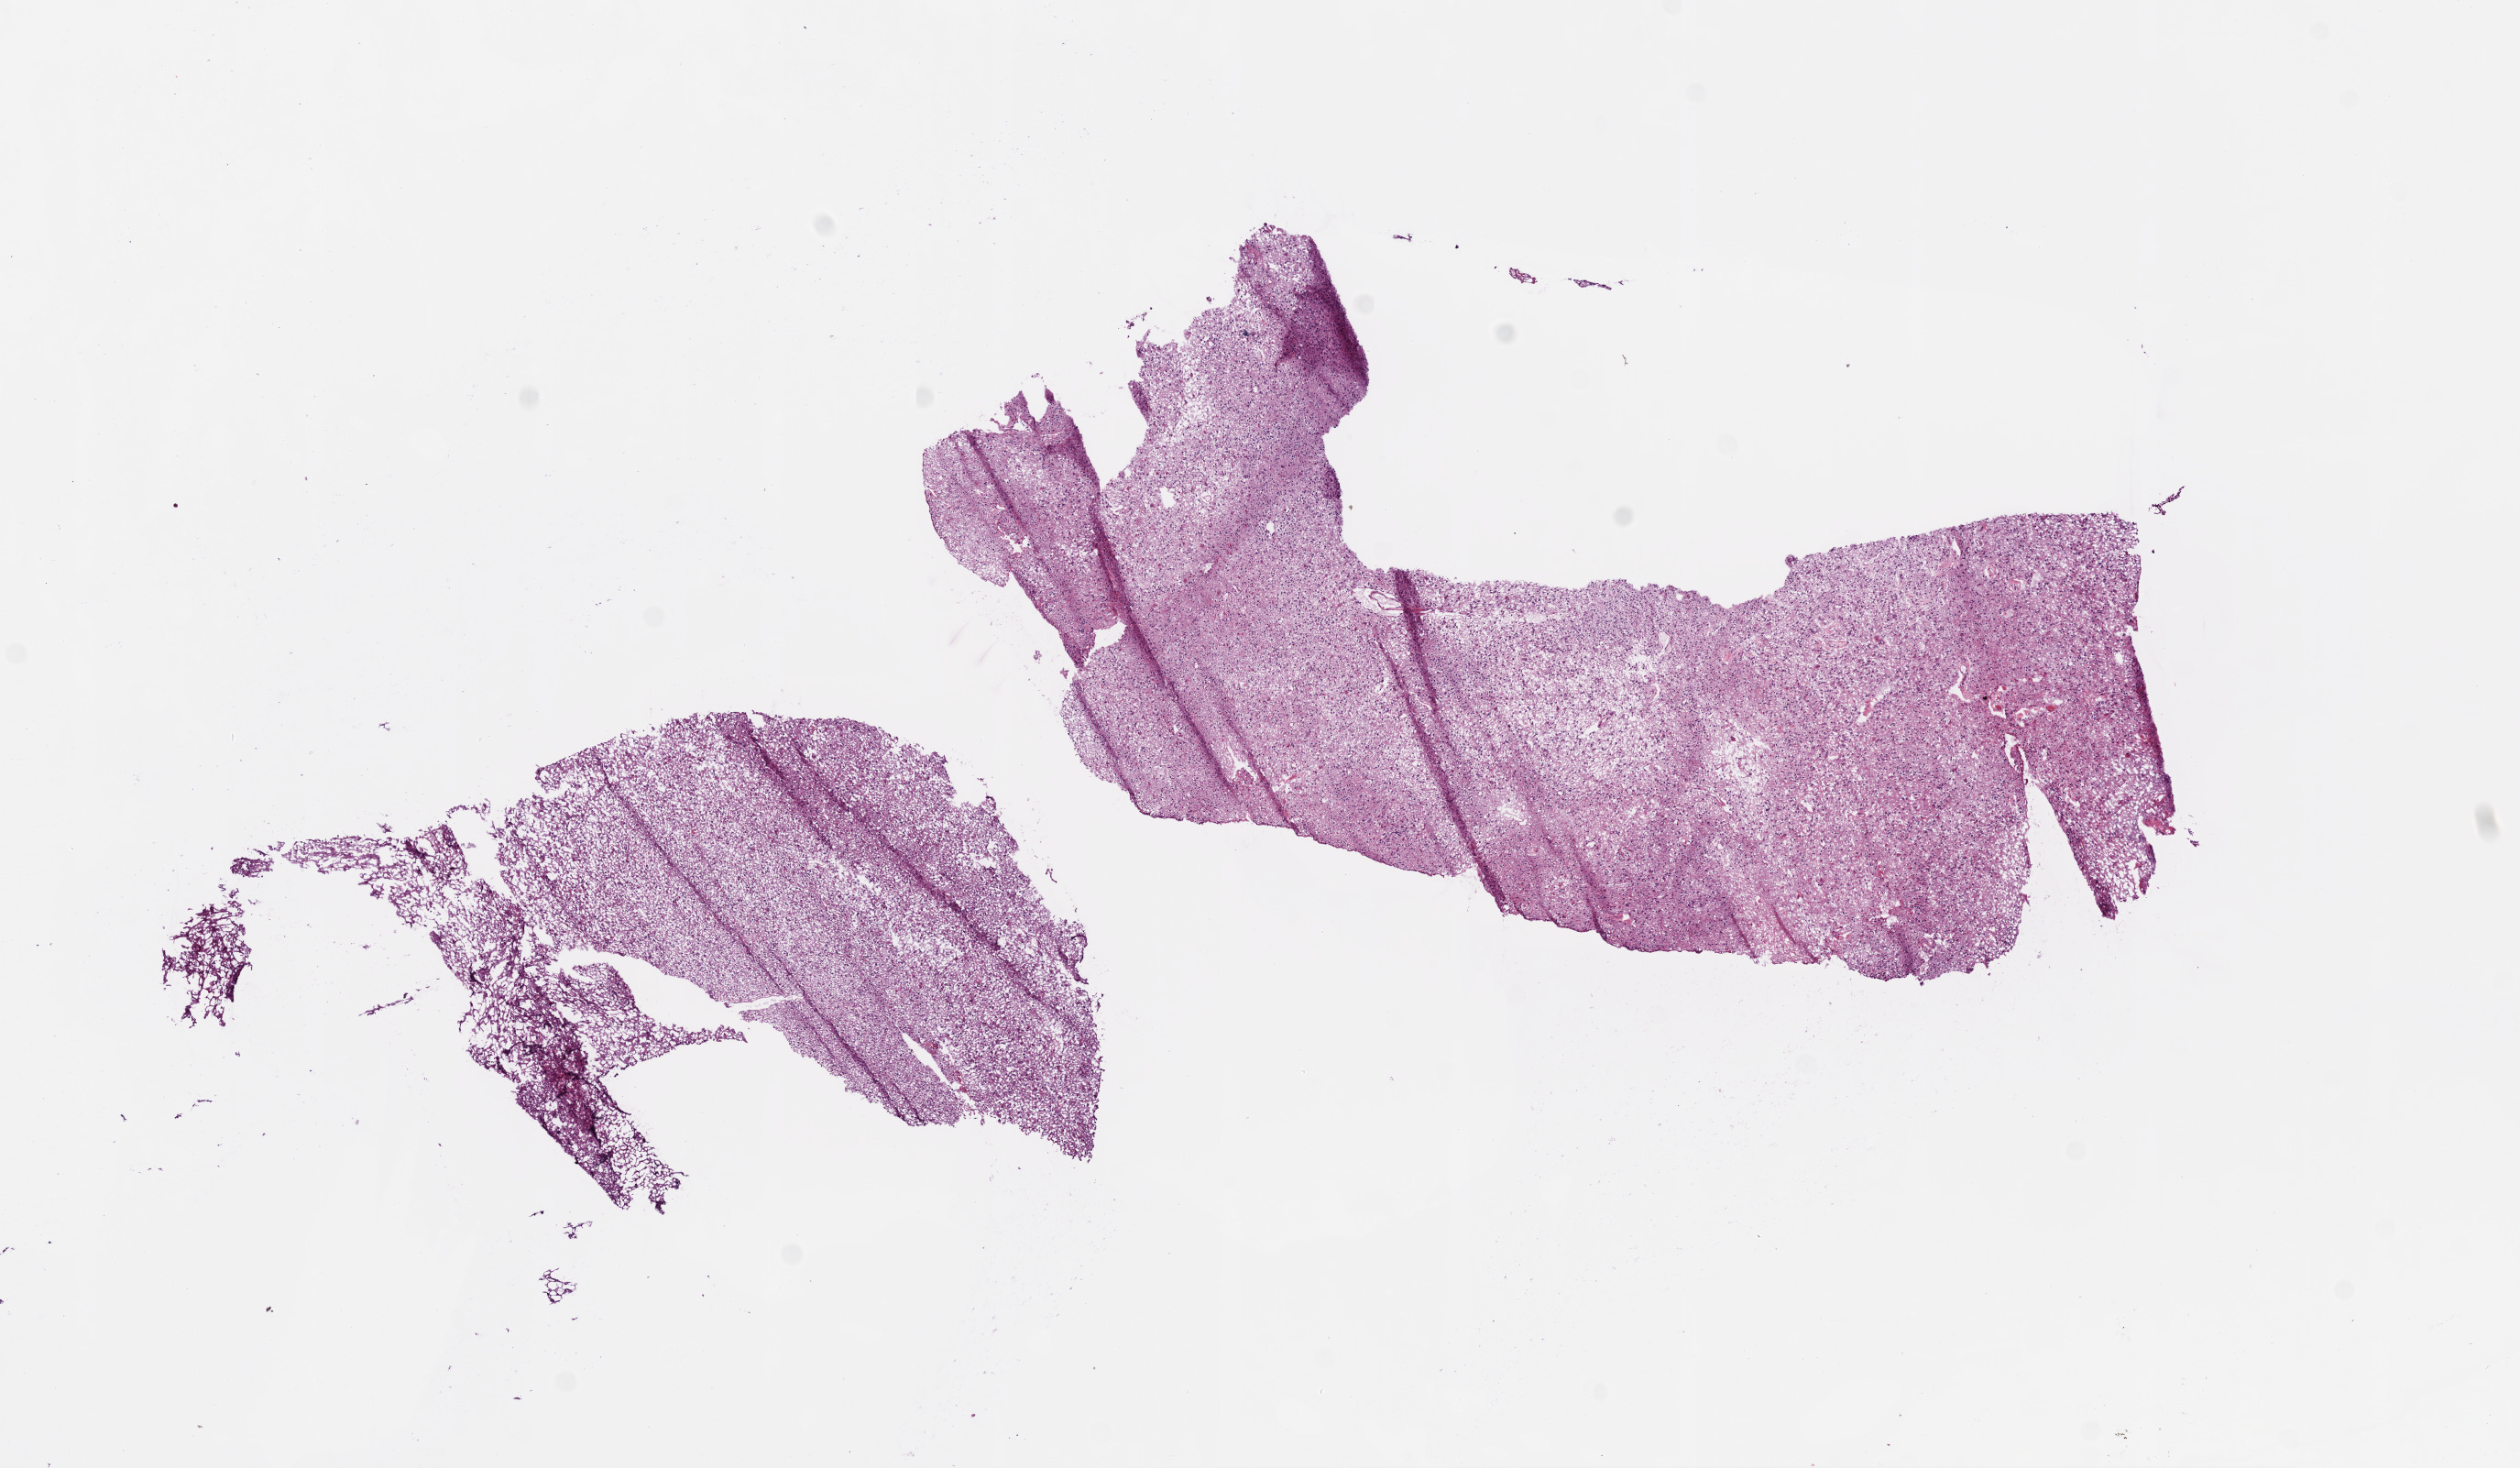
H&E-stained whole-slide image, shown as a low-resolution overview of the whole scanned area (about 11.0 x 6.4 mm), frozen section from the bottom of the tissue portion, primary tumour sample from the brain. Female, age 59 years at initial diagnosis. Pathologist review of this section (percent, as recorded): tumour cells 80%, tumour nuclei 90%, normal cells 10%, stromal cells 5%, necrosis 5%.
* pathologic diagnosis: Glioblastoma